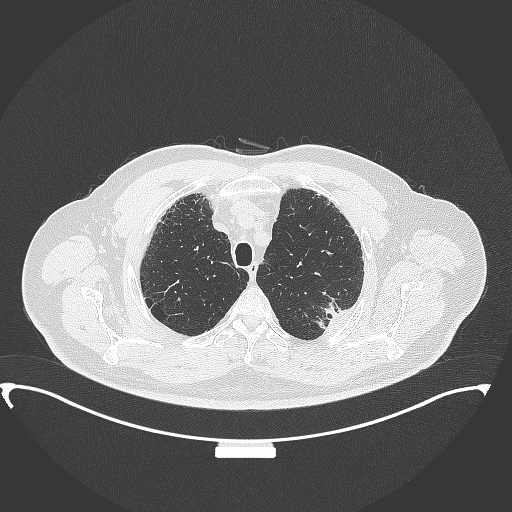
Chest CT, one axial slice; position 299 of 350 along the scan axis; reconstruction kernel B70f; 120 kVp; lung window (W 1500 / L -600 HU); 1 mm slice thickness; 512 × 512 image matrix. Patient: male, 64 years. Case-level facts recorded for this patient, not image findings: clinical TNM (as recorded): T1c N1 M1.
Annotated regions visible in this slice (rectangle marked by the reading radiologist):
- lung tumour (recorded histology: adenocarcinoma): box from (x=309, y=296) to (x=349, y=335) px